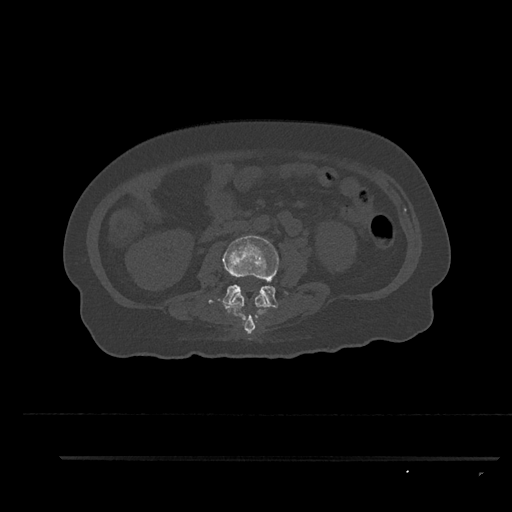
CT including the spine, one axial slice; position 113 of 797 along the scan axis; reconstruction kernel Br40s/3; 120 kVp; bone window (W 1800 / L 400 HU); 0.5 mm slice thickness; 512 × 512 image matrix, field of view 408 × 408 mm. Female patient, age 44 years. From the clinical record (not read from this slice): primary cancer: renal; vertebrae with lytic lesions (as recorded): L1.
Structures marked on this image (semi-automatically segmented with operator editing):
- L2 vertebra: bounding box <225,293,268,334> (left, top, right, bottom; pixels)
- L3 vertebra: <218,235,288,308>